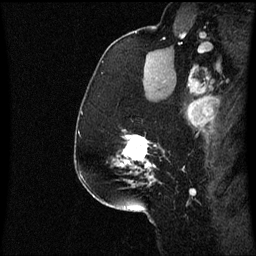
Breast MRI (dynamic contrast-enhanced), one sagittal slice; position 44 of 60 along the scan axis; dynamic contrast-enhanced series, image 2 of 3 at this slice position (ordered by acquisition); 1.5 T; TE 4.2 ms, TR 8.9 ms; 2 mm slice thickness; 256 × 256 image matrix, field of view 200 × 200 mm. Female patient, age 58 years. From the clinical record (not read from this slice): setting: breast cancer imaged before/during neoadjuvant chemotherapy; receptor status: triple-negative.
Structures marked on this image (semi-automatic segmentation, software-assisted and operator-edited):
- analysis volume of interest (the breast-tissue region the enhancement analysis was run in; not a lesion): bounding box <108,130,165,179> (left, top, right, bottom; pixels)
- tumour enhancement mask (voxels above the 70 % enhancement threshold inside the analysis volume of interest): <122,130,155,179>